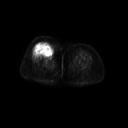
FDG PET of an extremity soft-tissue mass (from a PET/CT study), one axial slice. Slice 32 of 267 in the series (ordered by position). 128 × 128 image matrix, field of view 700 × 700 mm. Patient: female, 56 years. Case-level facts recorded for this patient, not image findings: histological type: malignant solitary fibrous tumor; grade: intermediate; site of the primary tumour: right thigh.
Structures marked on this image (expert contour drawn on MRI and transferred to this co-registered scan by the dataset authors):
- gross tumour volume including surrounding oedema: bounding box (x1, y1, x2, y2) in pixels: (34, 41, 55, 58)
- gross tumour volume (mass): (35, 41, 55, 57)